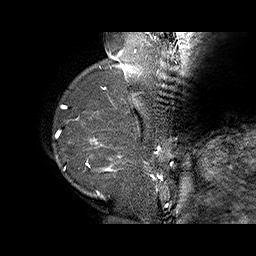
Breast MRI (dynamic contrast-enhanced), one sagittal slice. Dynamic contrast-enhanced series, time point 2 of 6 at this slice position (early post-contrast). 1.5 T. TE 4.5 ms, TR 32.4 ms. 3 mm slice thickness. 256 × 256 image matrix. Female patient. From the clinical record (not read from this slice): setting: breast cancer imaged before/during neoadjuvant chemotherapy; receptor status: HR-positive, HER2-negative.
Annotated regions visible in this slice (semi-automatic segmentation, software-assisted and operator-edited):
- analysis volume of interest (the breast-tissue region the enhancement analysis was run in; not a lesion): bounding box [x1, y1, x2, y2] px = [71, 128, 159, 202]
- tumour enhancement mask (voxels above the 100 % enhancement threshold inside the analysis volume of interest): [86, 137, 159, 195]